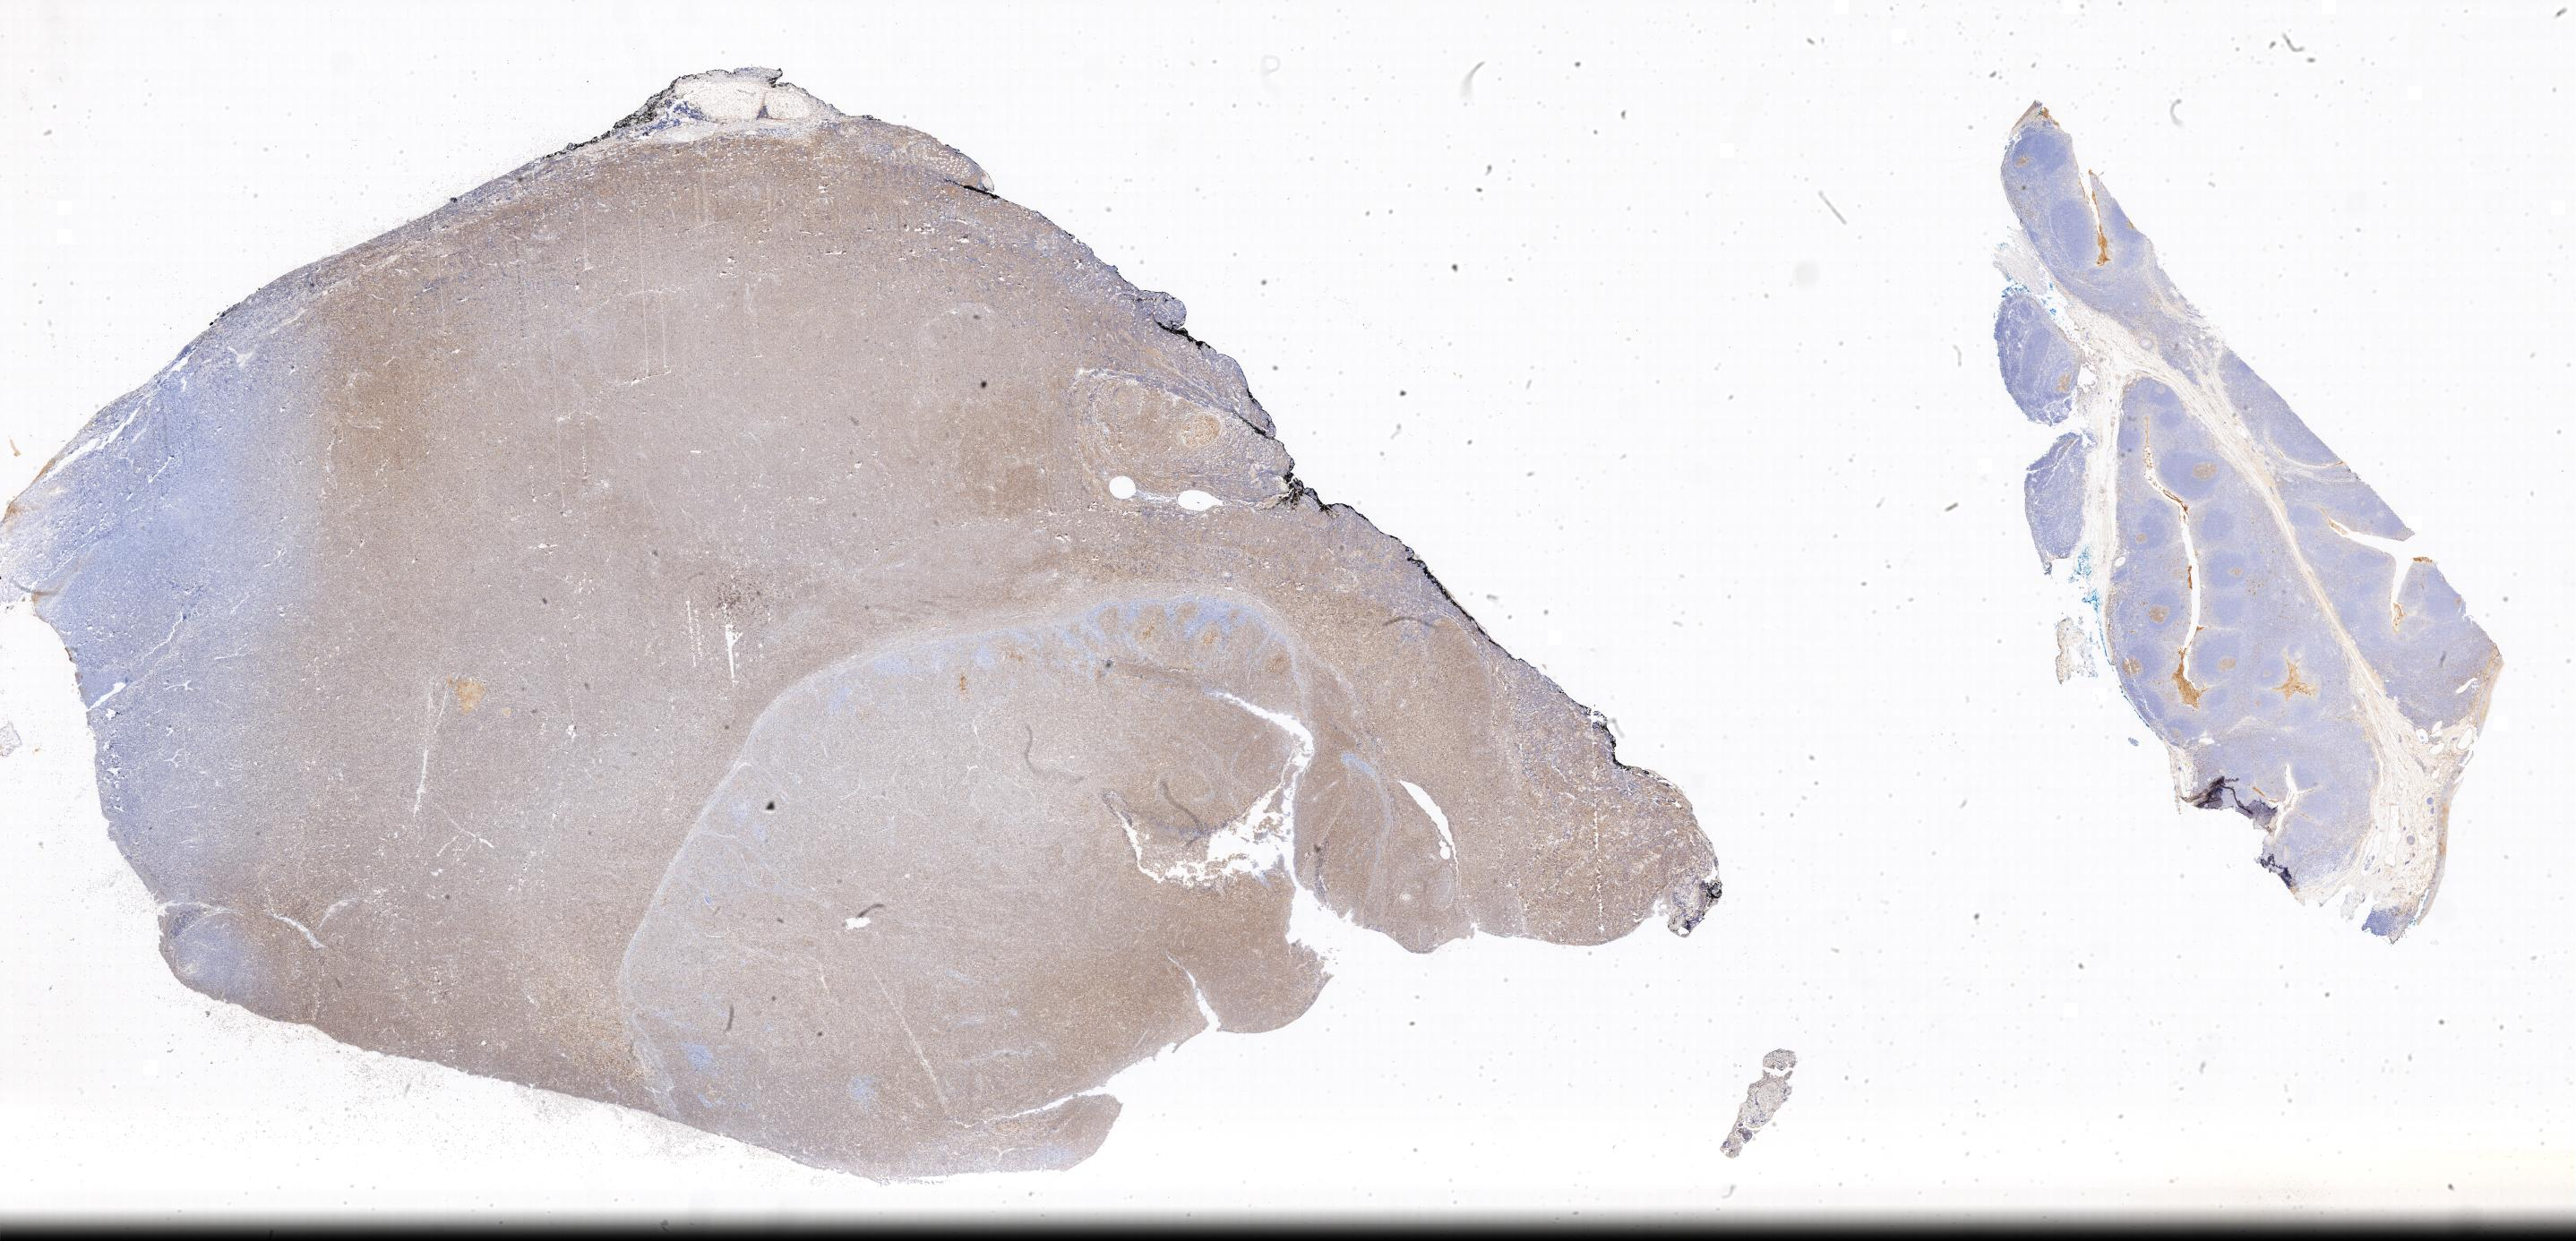
IHC for CD10, whole-slide image, shown as a low-resolution overview of the whole scanned area; specimen: tumor tissue; anatomic site: lymph node of head and neck. Patient: male, age at initial diagnosis 6 years.
• histologic diagnosis: Burkitt lymphoma, NOS